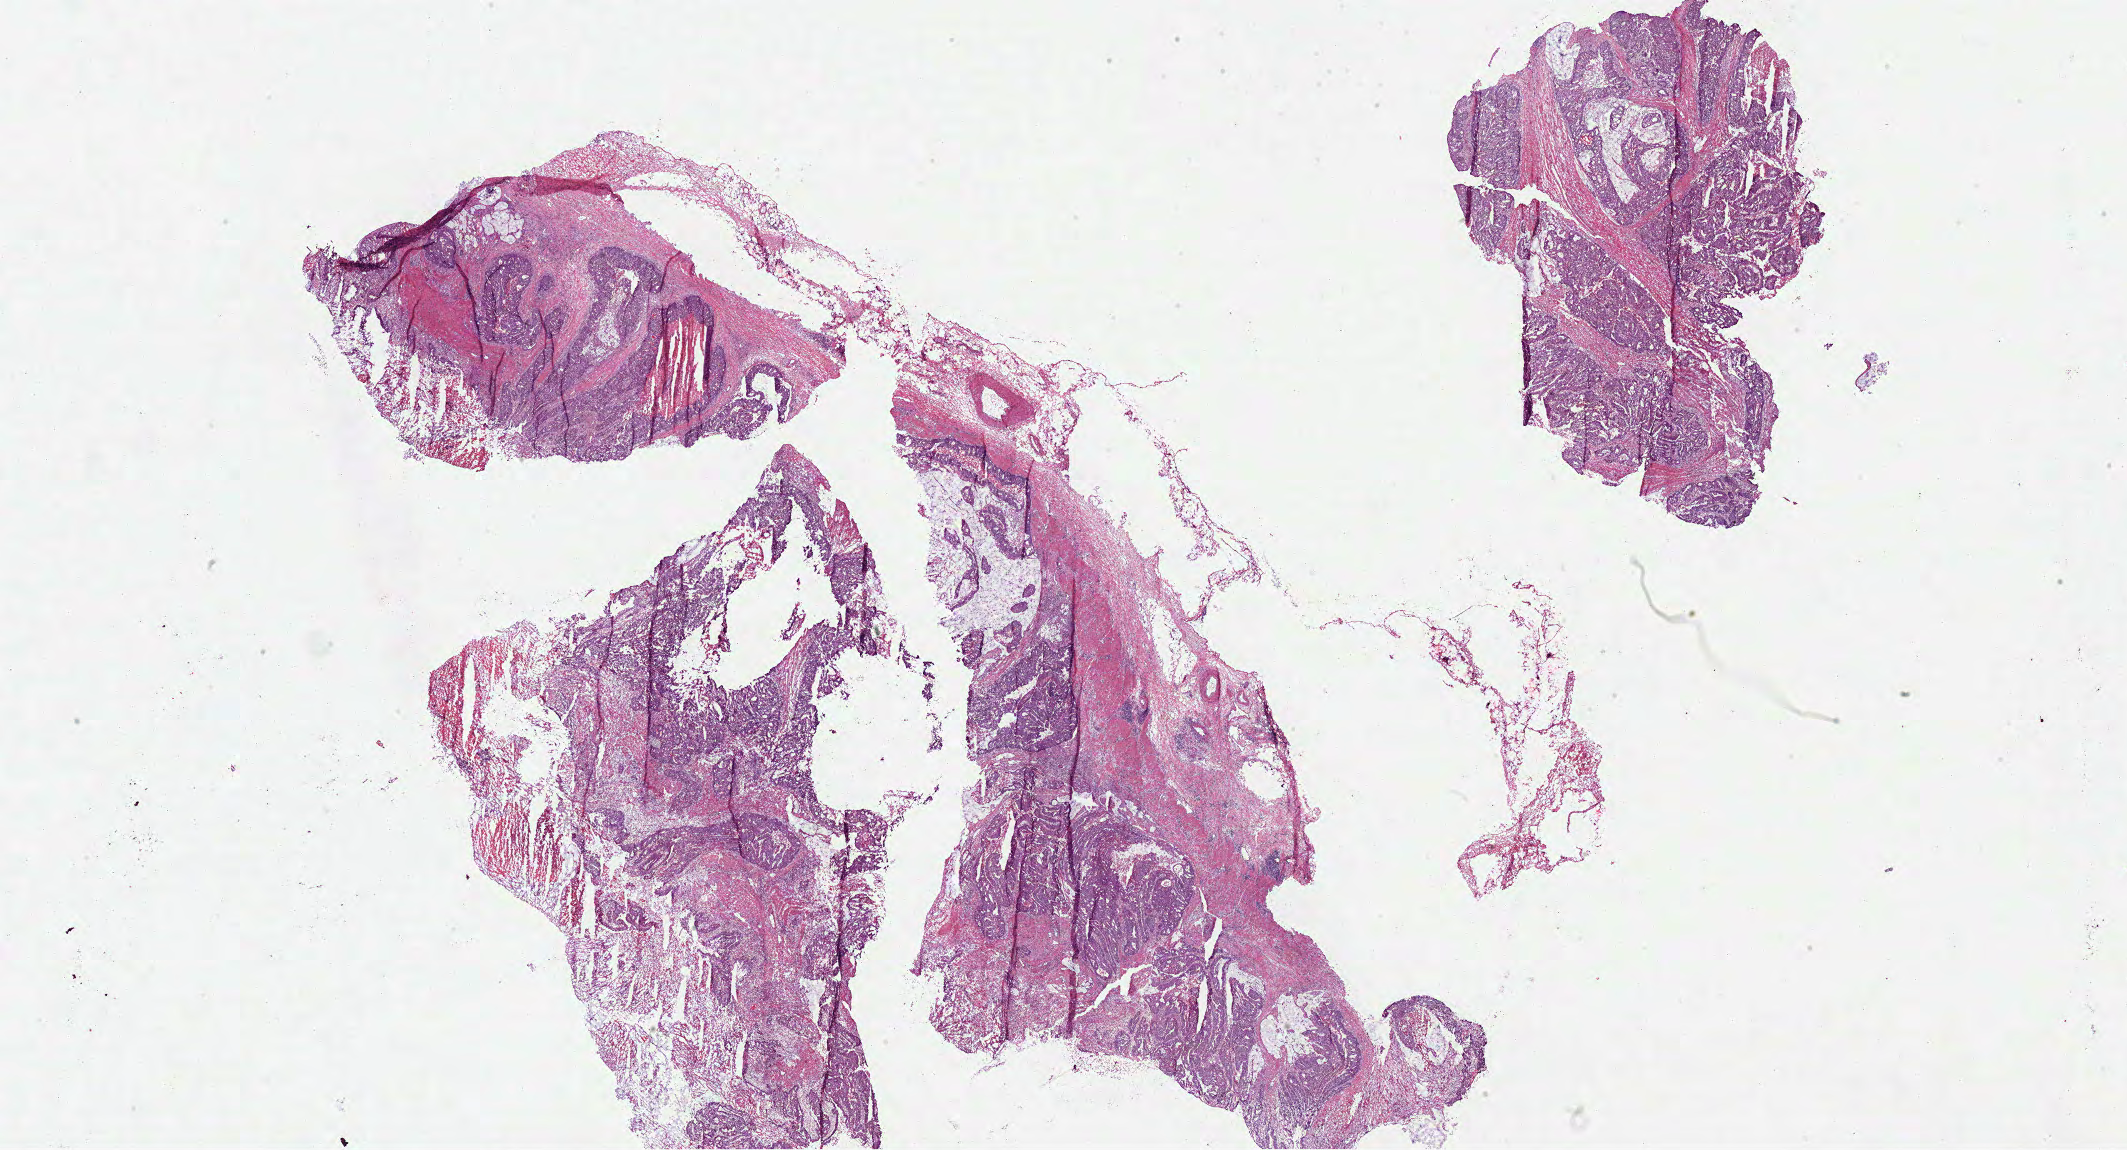
Digitized Hematoxylin and eosin (H&E) stained tissue section (whole slide), shown as a low-resolution overview of the whole scanned area (about 33.5 x 18.1 mm, slide scanned at 40x). Frozen section from the bottom of the tissue portion. Primary tumour sample from the colon. Male patient; age at initial diagnosis 51 years. Pathologist review of this section (percent, as recorded): tumour cells 82%, tumour nuclei 80%, normal cells 0%, stromal cells 0%, necrosis 18%. Inflammatory infiltration, as recorded: lymphocyte infiltration 2%, monocyte infiltration 0%, neutrophil infiltration 1%.
- diagnosis: Mucinous adenocarcinoma (transverse colon)
- AJCC pathologic stage: IIA (7th edition)